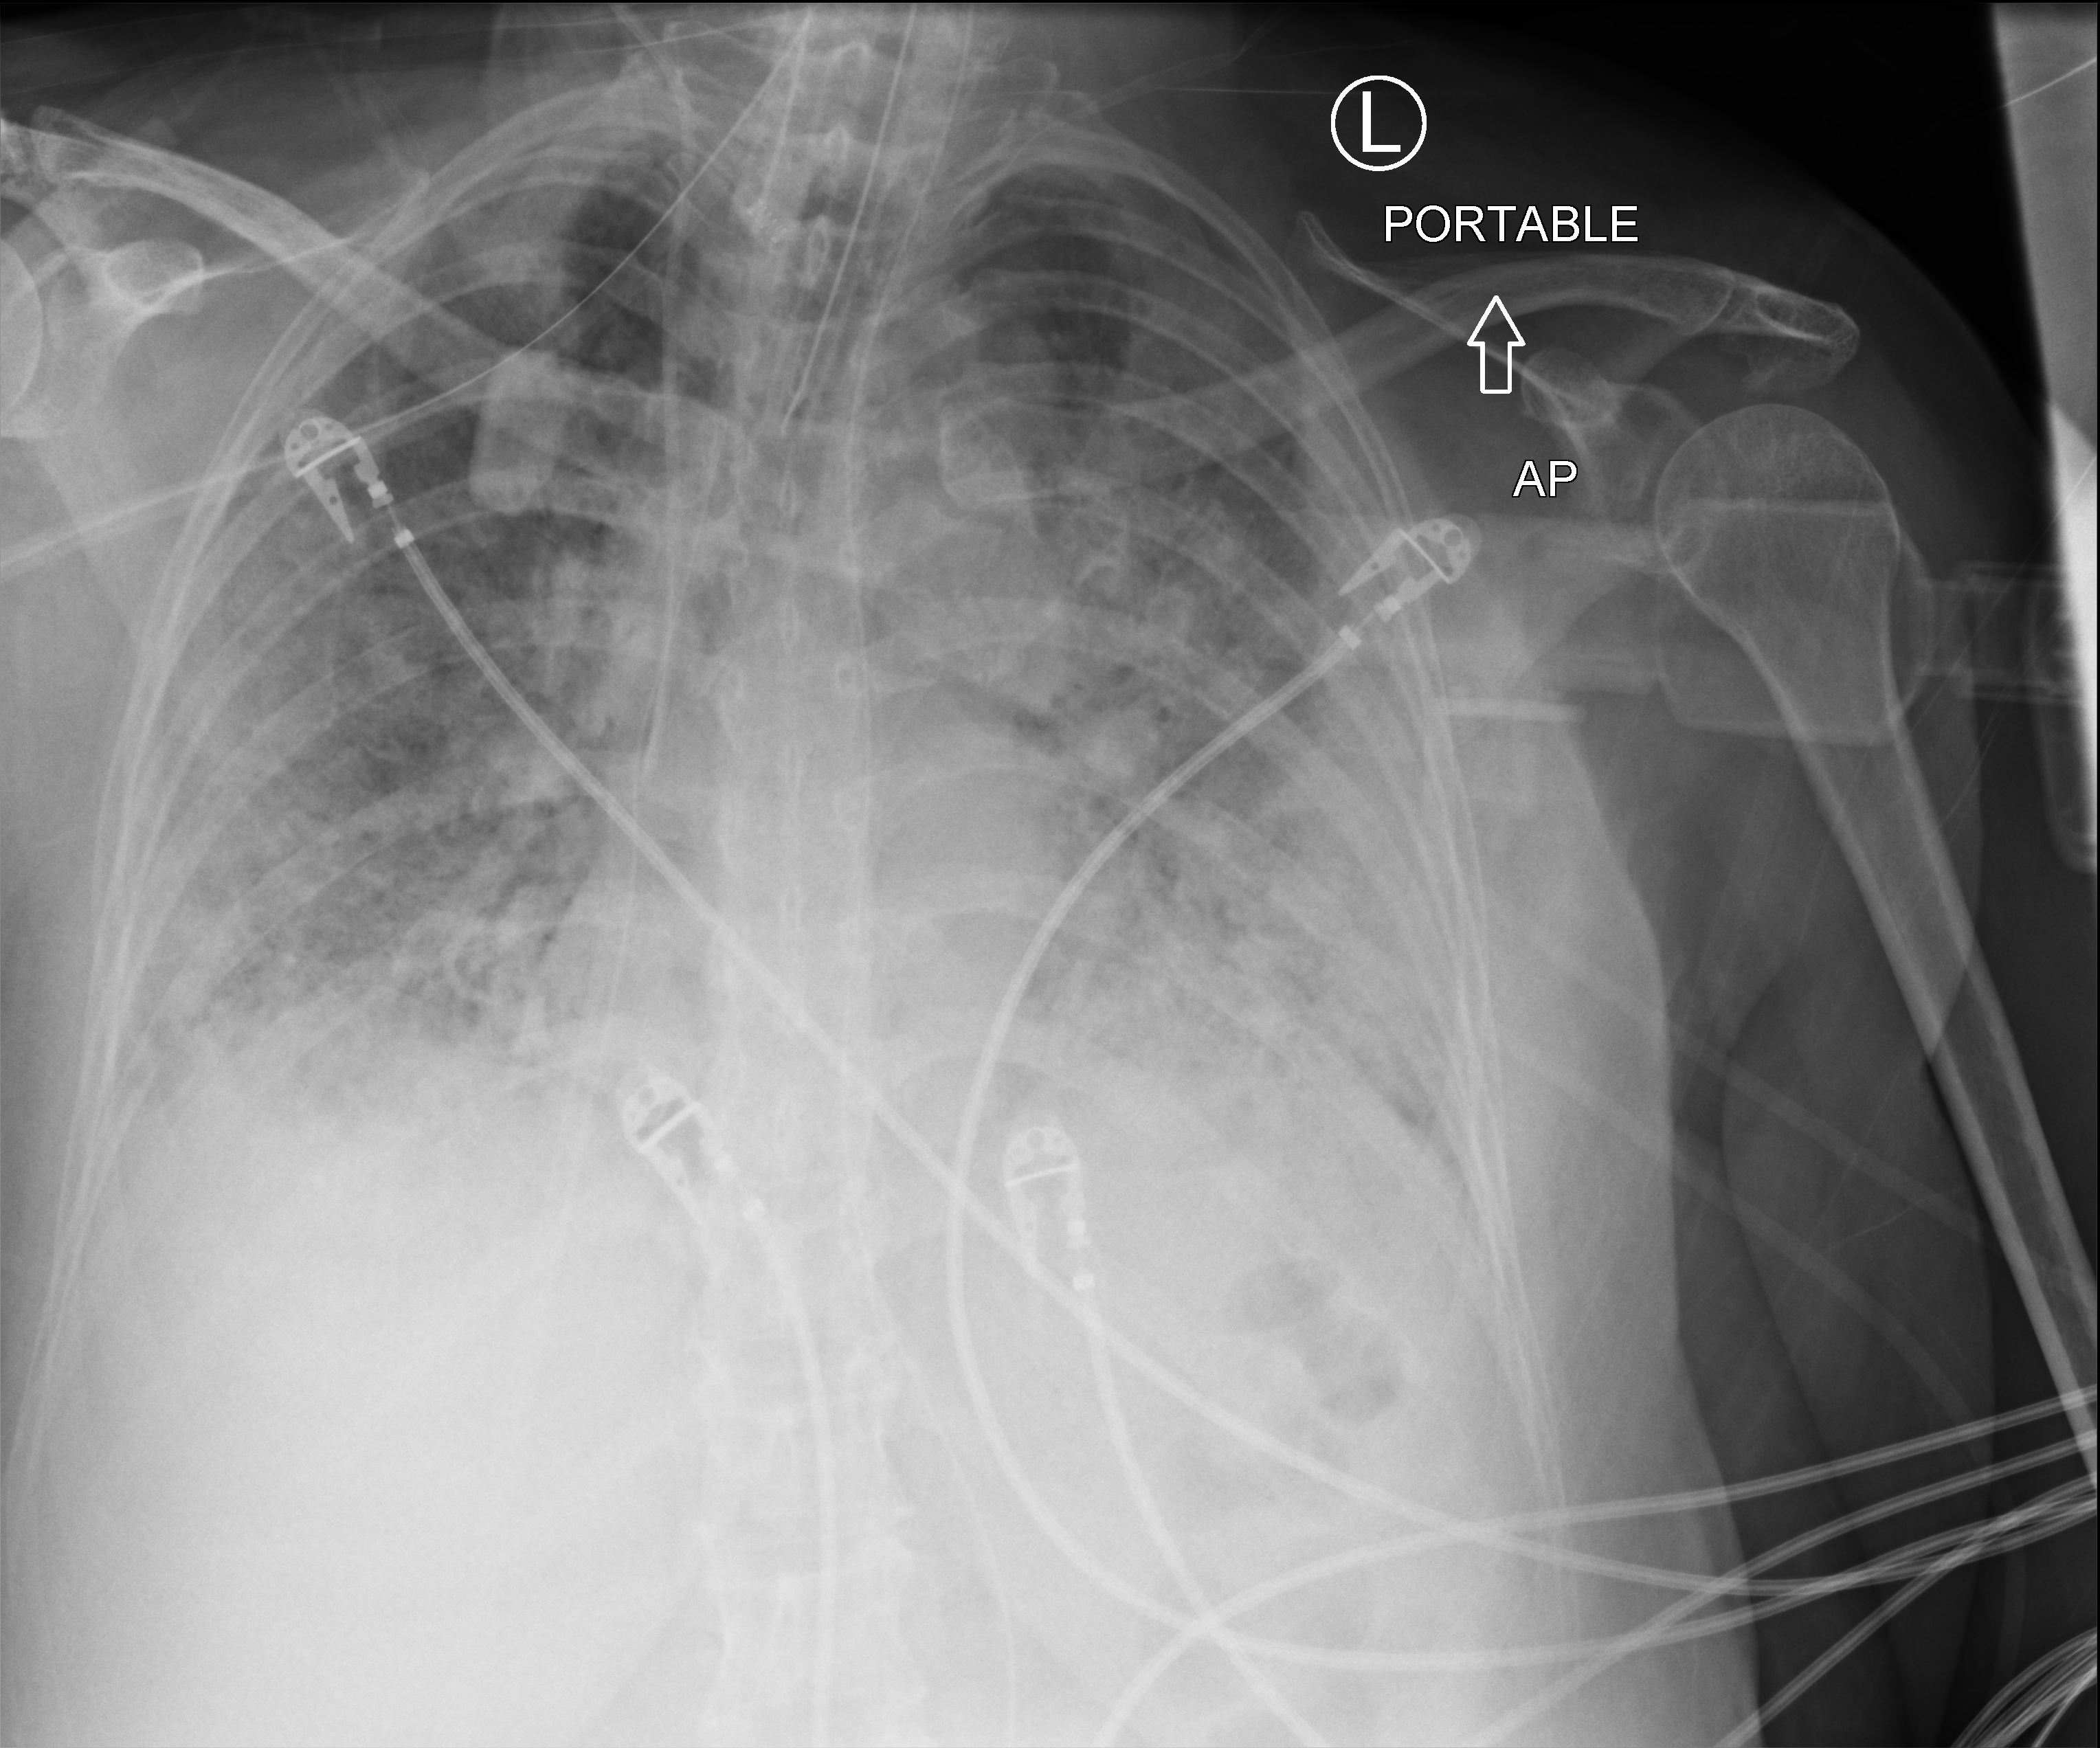
Chest X-ray (portable), anteroposterior (AP) projection. Female patient hospitalised with COVID-19, age 60–74 years.
Admission-level facts for this patient (not findings on this image; timing relative to this image not recorded): COPD (admission record): no; admitted to intensive care during this hospital stay: yes.